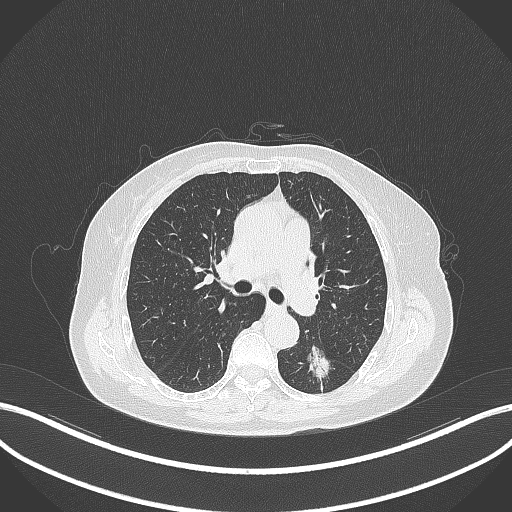
Chest CT, one axial slice; reconstruction kernel B70f; lung window (W 1500 / L -600 HU); 1 mm slice thickness; 512 × 512 image matrix. Female patient, age 70 years. Case-level facts recorded for this patient, not image findings: clinical TNM (as recorded): T1c N0 M0.
Annotated regions visible in this slice (bounding box drawn by a radiologist):
- lung tumour (recorded histology: adenocarcinoma): bounding box [x1, y1, x2, y2] px = [300, 339, 333, 381]